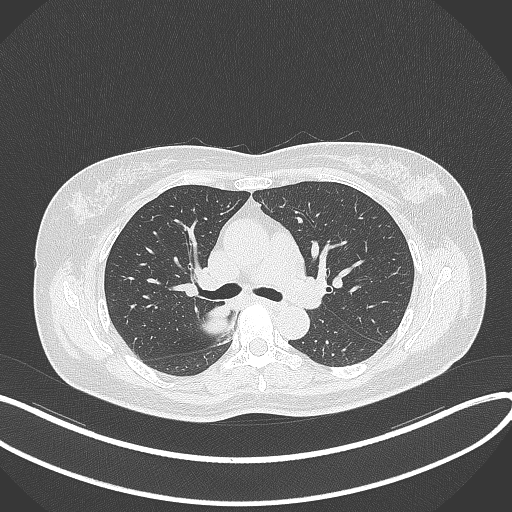
Chest CT, one axial slice; reconstruction kernel B70f; 120 kVp; lung window (W 1500 / L -600 HU); 512 × 512 image matrix. Patient: female, 54 years. From the clinical record (not read from this slice): clinical TNM (as recorded): T4 N0 M0.
Annotated regions visible in this slice (bounding box drawn by a radiologist):
- lung tumour (recorded histology: adenocarcinoma): bounding box [x1, y1, x2, y2] px = [201, 301, 232, 340]